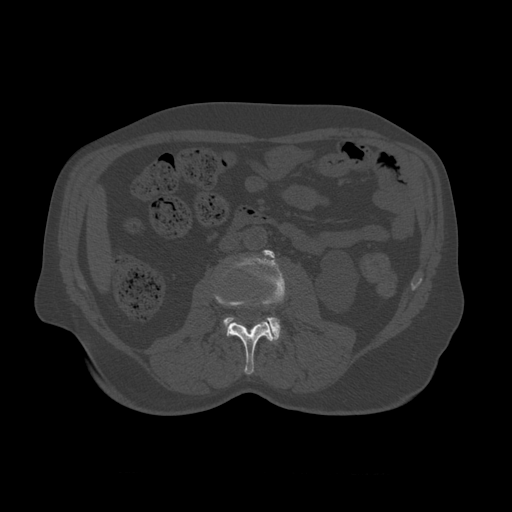
CT including the spine, one axial slice; position 320 of 450 along the scan axis; 120 kVp; bone window (W 1800 / L 400 HU); 1.25 mm slice thickness; 512 × 512 image matrix, field of view 405 × 405 mm. Patient age 75 years. Case-level facts recorded for this patient, not image findings: primary cancer: prostate.
Outlined on this slice (semi-automatic segmentation, software-assisted and operator-edited):
- L2 vertebra: bounding box [x1, y1, x2, y2] px = [214, 292, 273, 375]
- L3 vertebra: [224, 250, 286, 344]